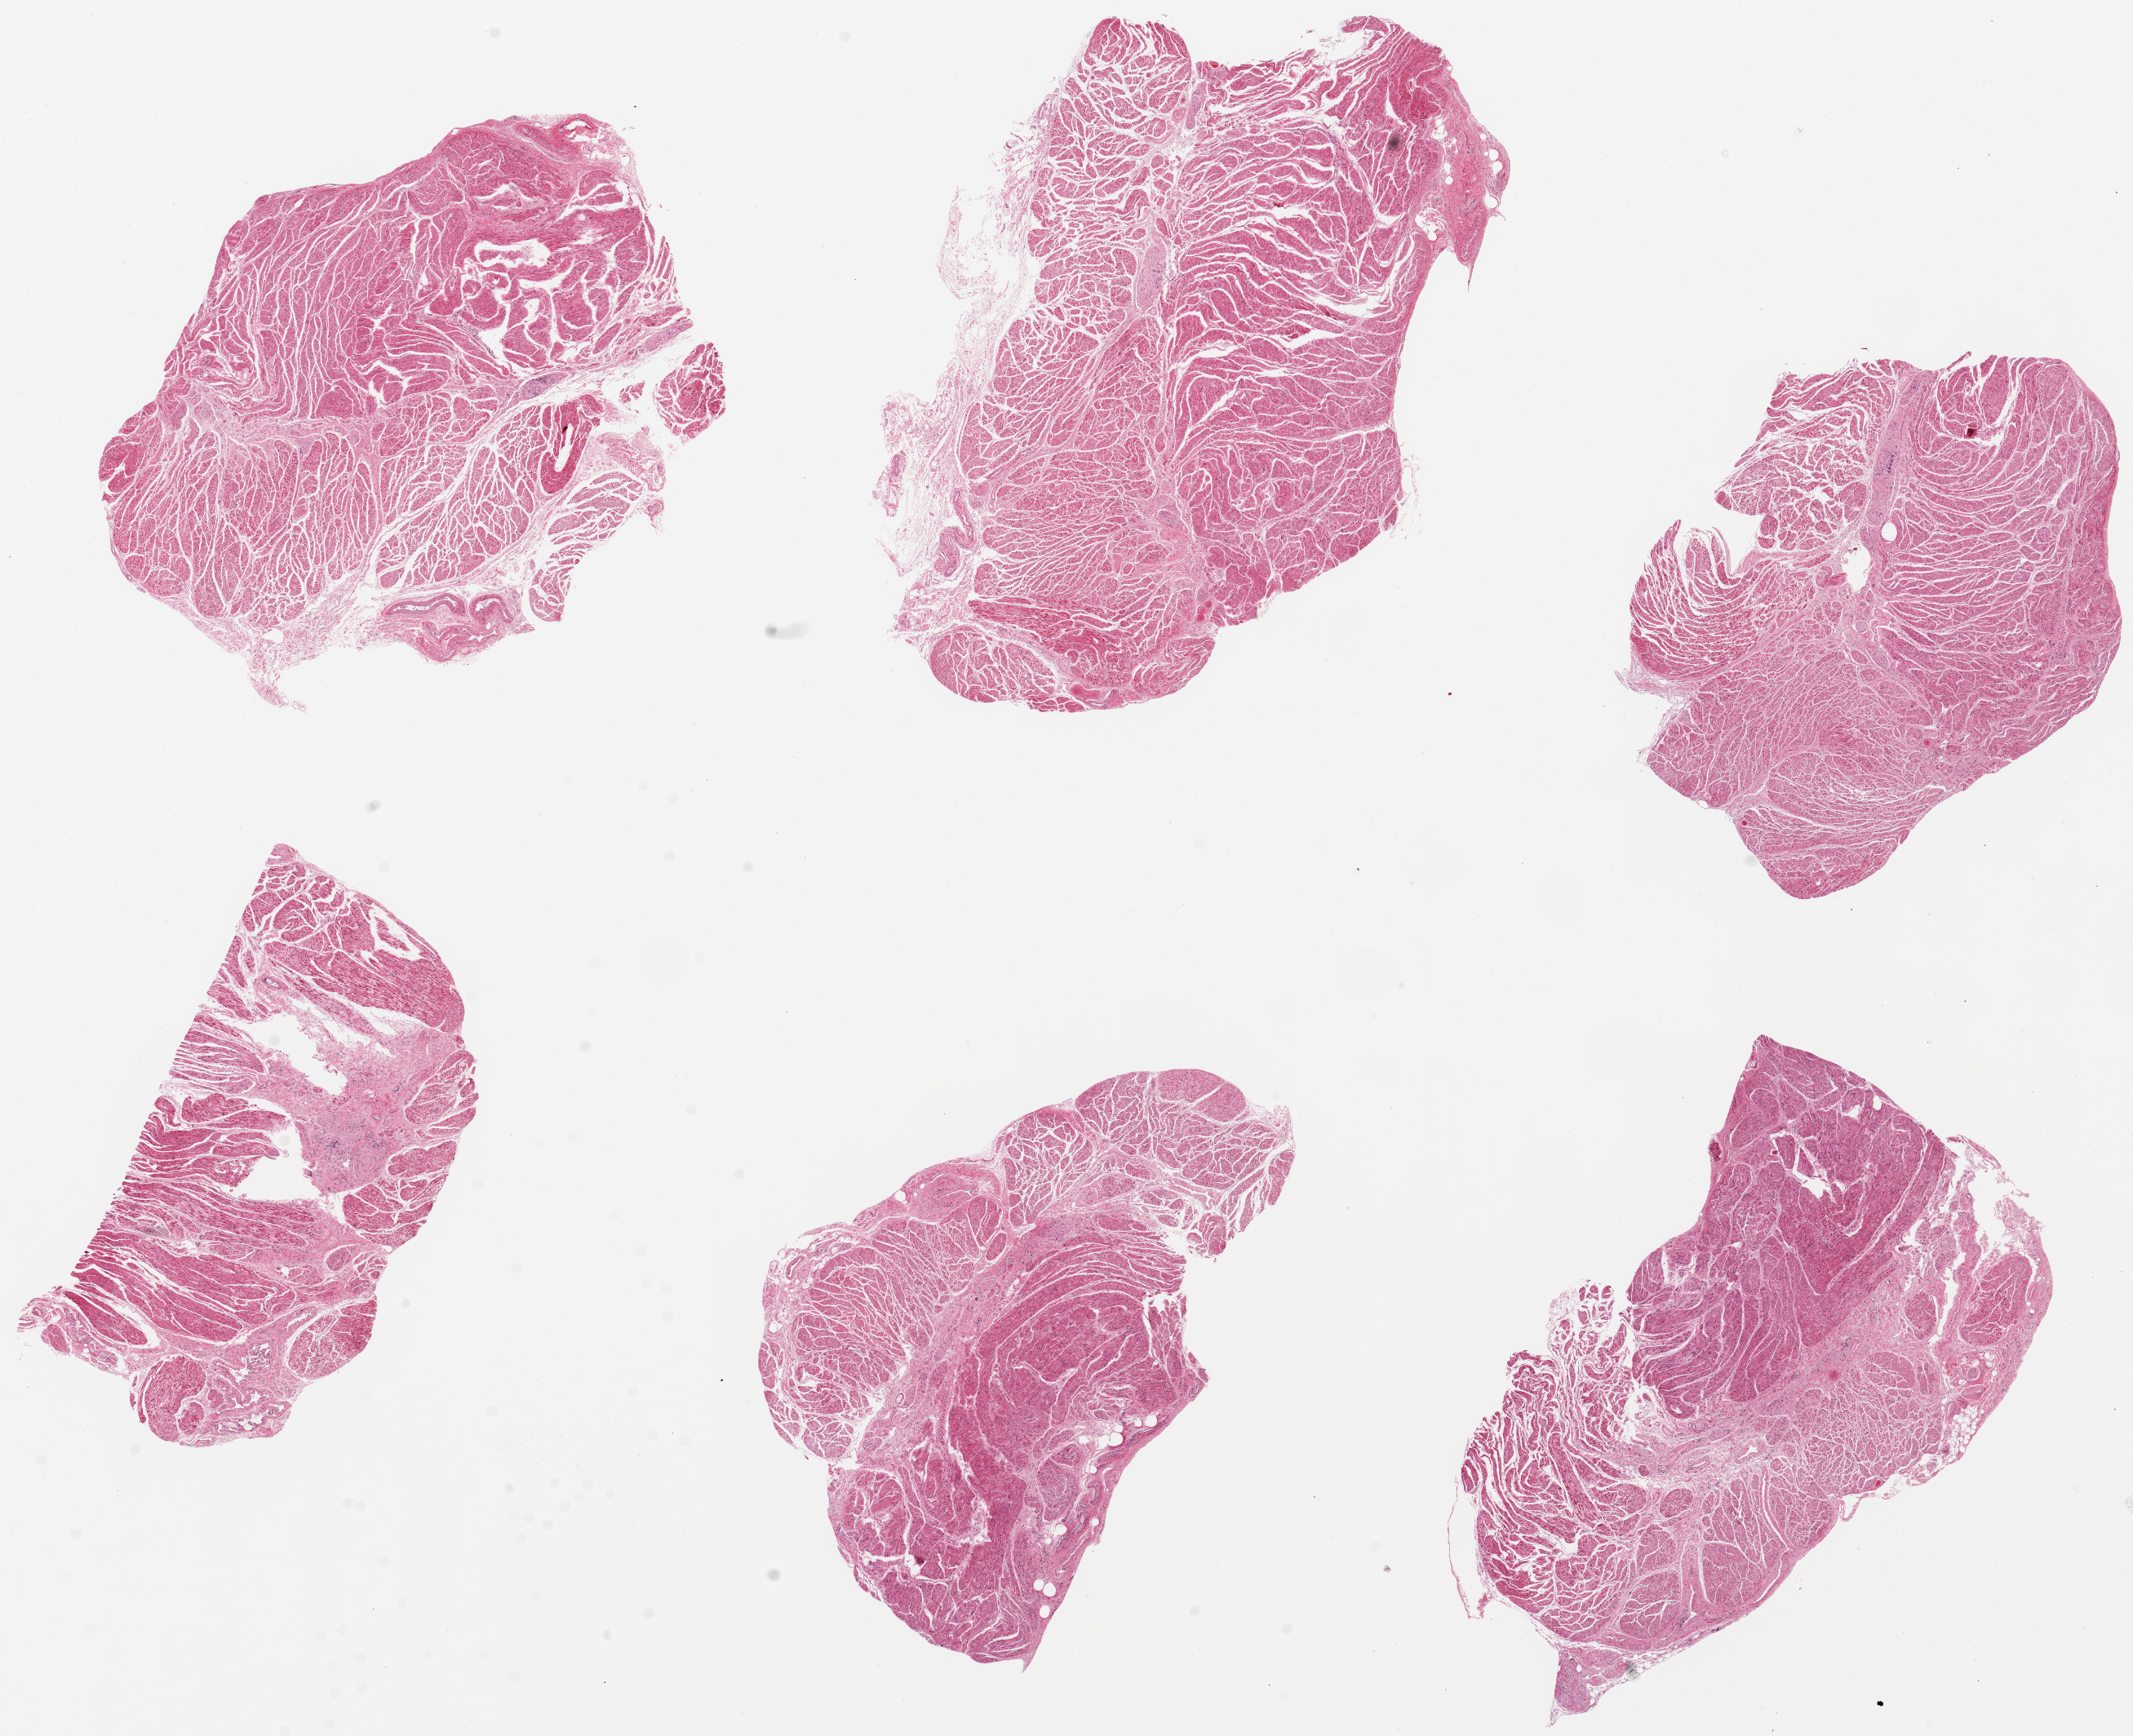
H&E whole-slide image, shown as a low-resolution overview of the whole scanned area (about 20.7 x 16.8 mm, slide scanned at 20x), PAXgene-fixed, paraffin-embedded tissue, target tissue: gastroesophageal junction, donor tissue sample.
Reviewer comment on this tissue sample: 6 pieces, up to 8x5mm; all muscle (good).